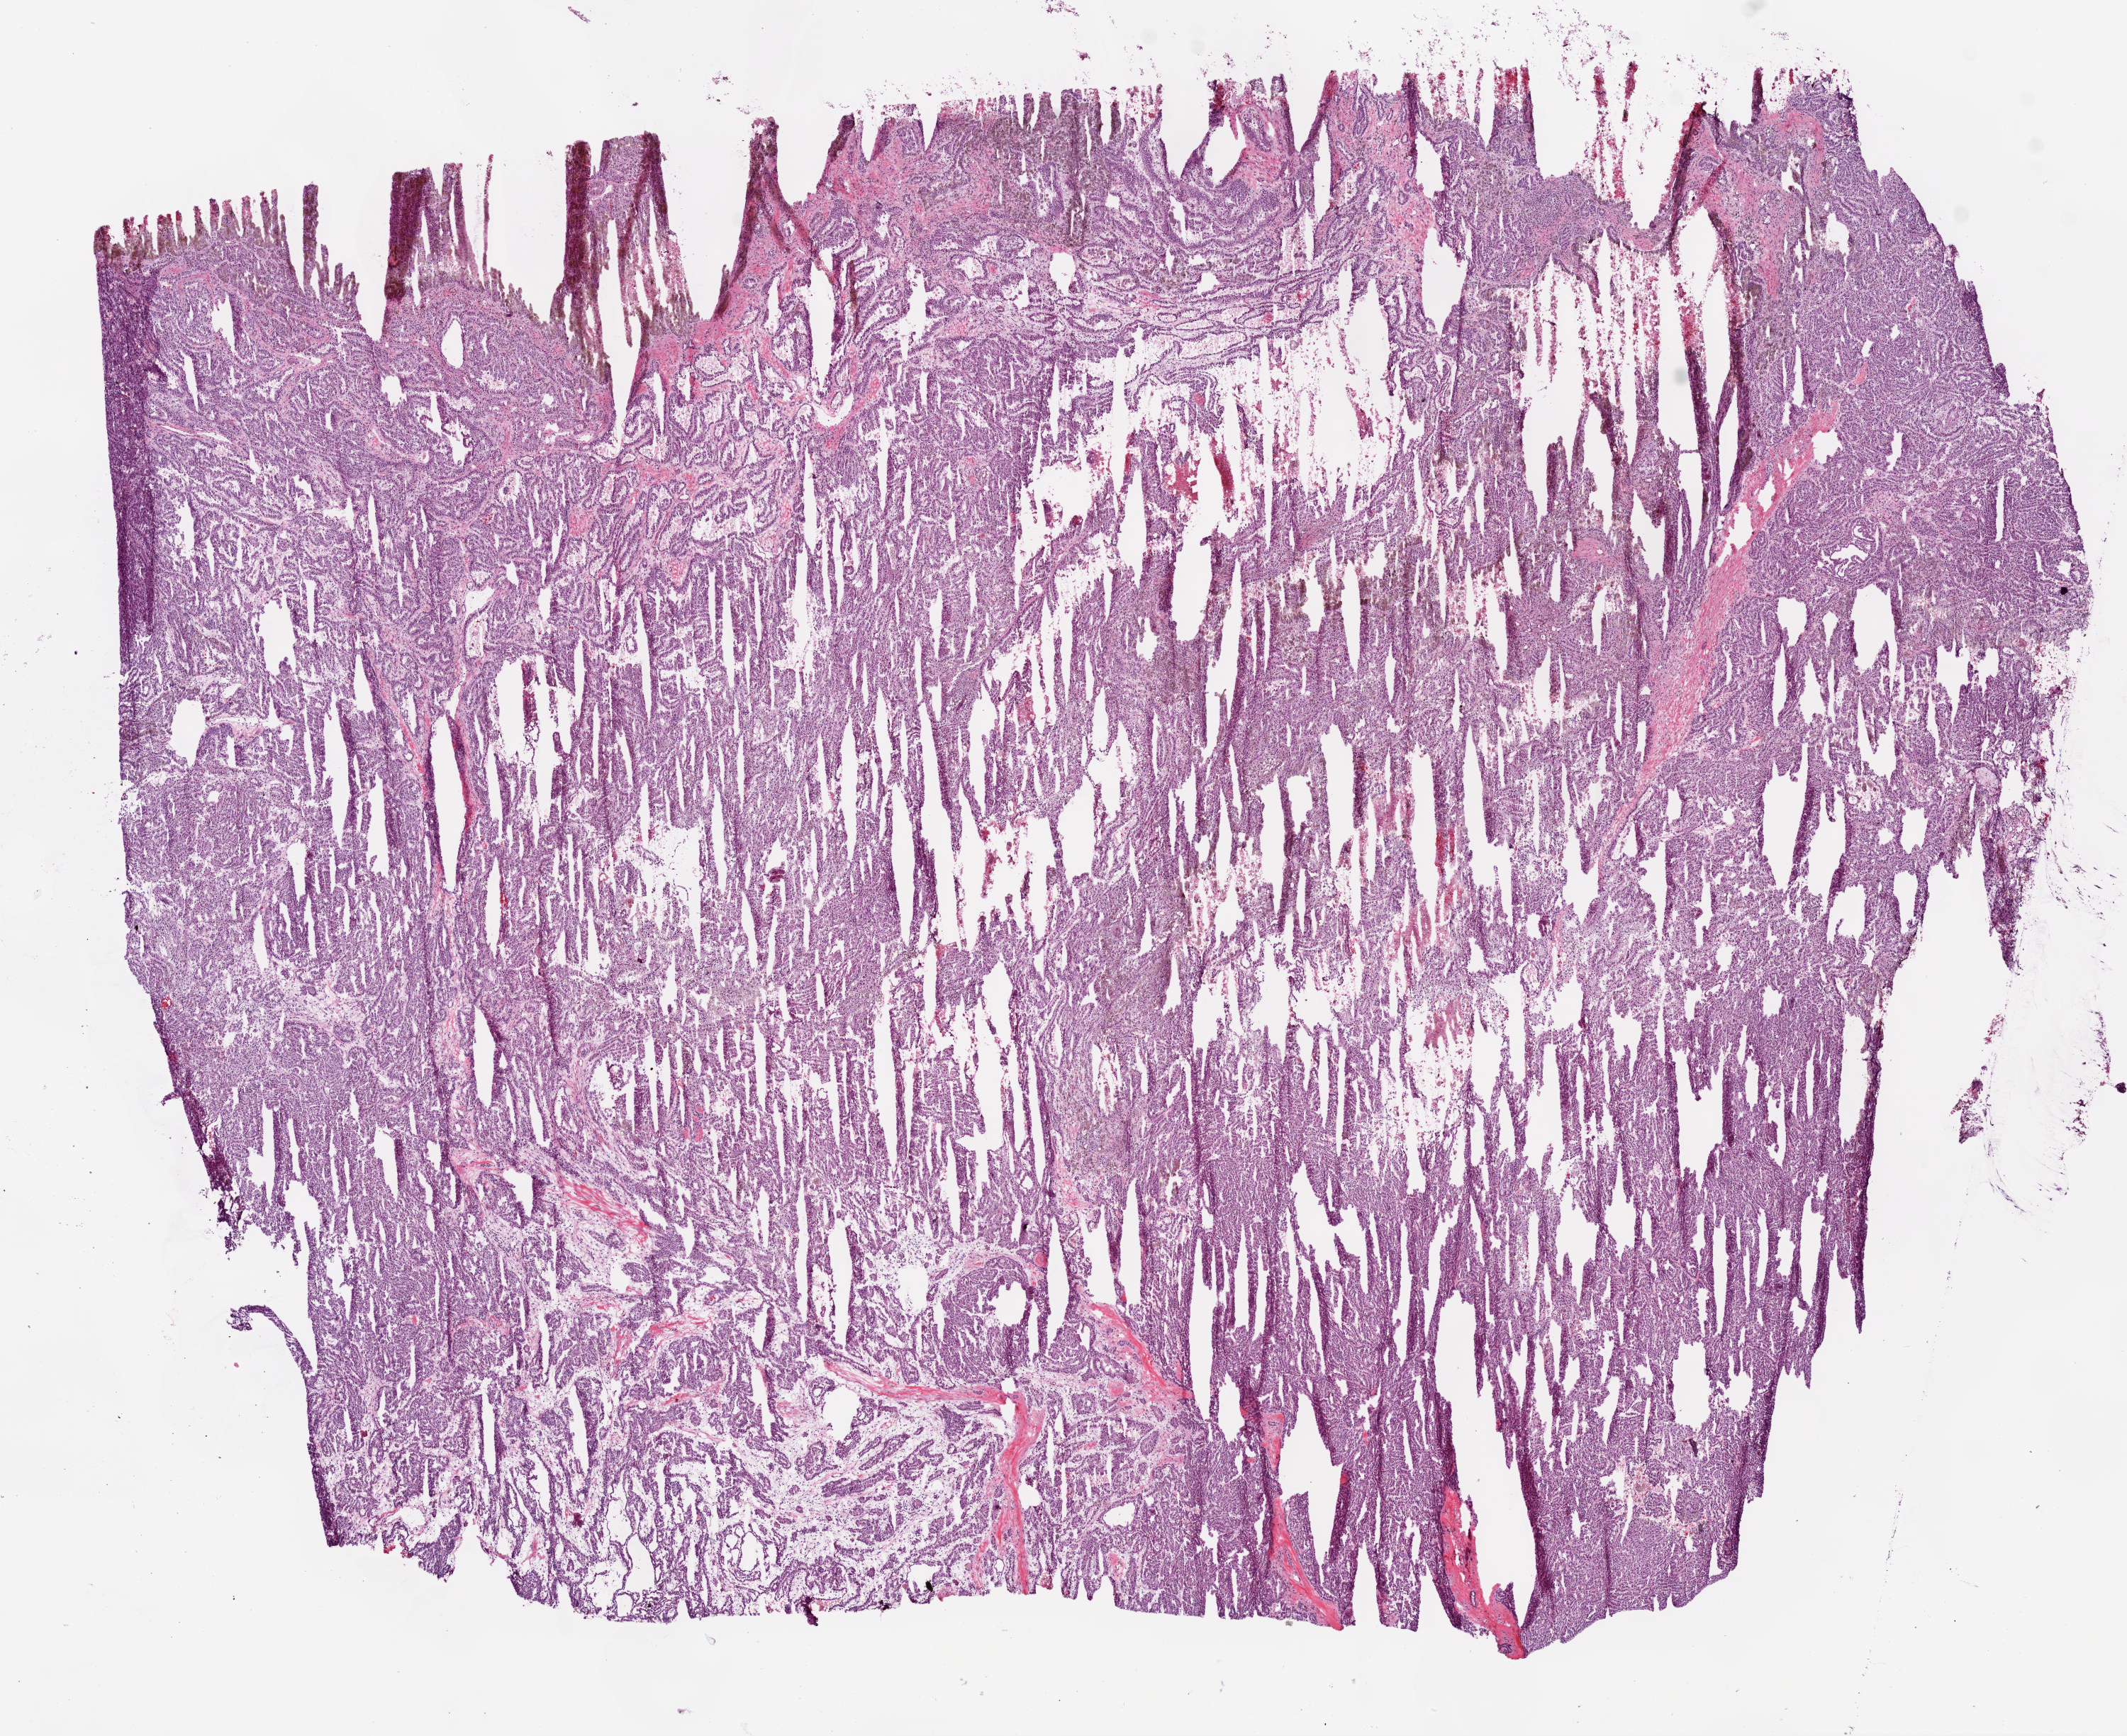
H&E whole-slide image, a low-resolution overview of the entire scanned area, about 12.0 x 9.8 mm; frozen section from the bottom of the tissue portion; primary tumour sample from the kidney. Male patient; age at initial diagnosis 56 years. Composition of this section per pathologist review: tumour cells 77%, tumour nuclei 85%, normal cells 3%, stromal cells 5%, necrosis 15%.
* histologic diagnosis: Papillary adenocarcinoma, NOS
* AJCC pathologic stage: I